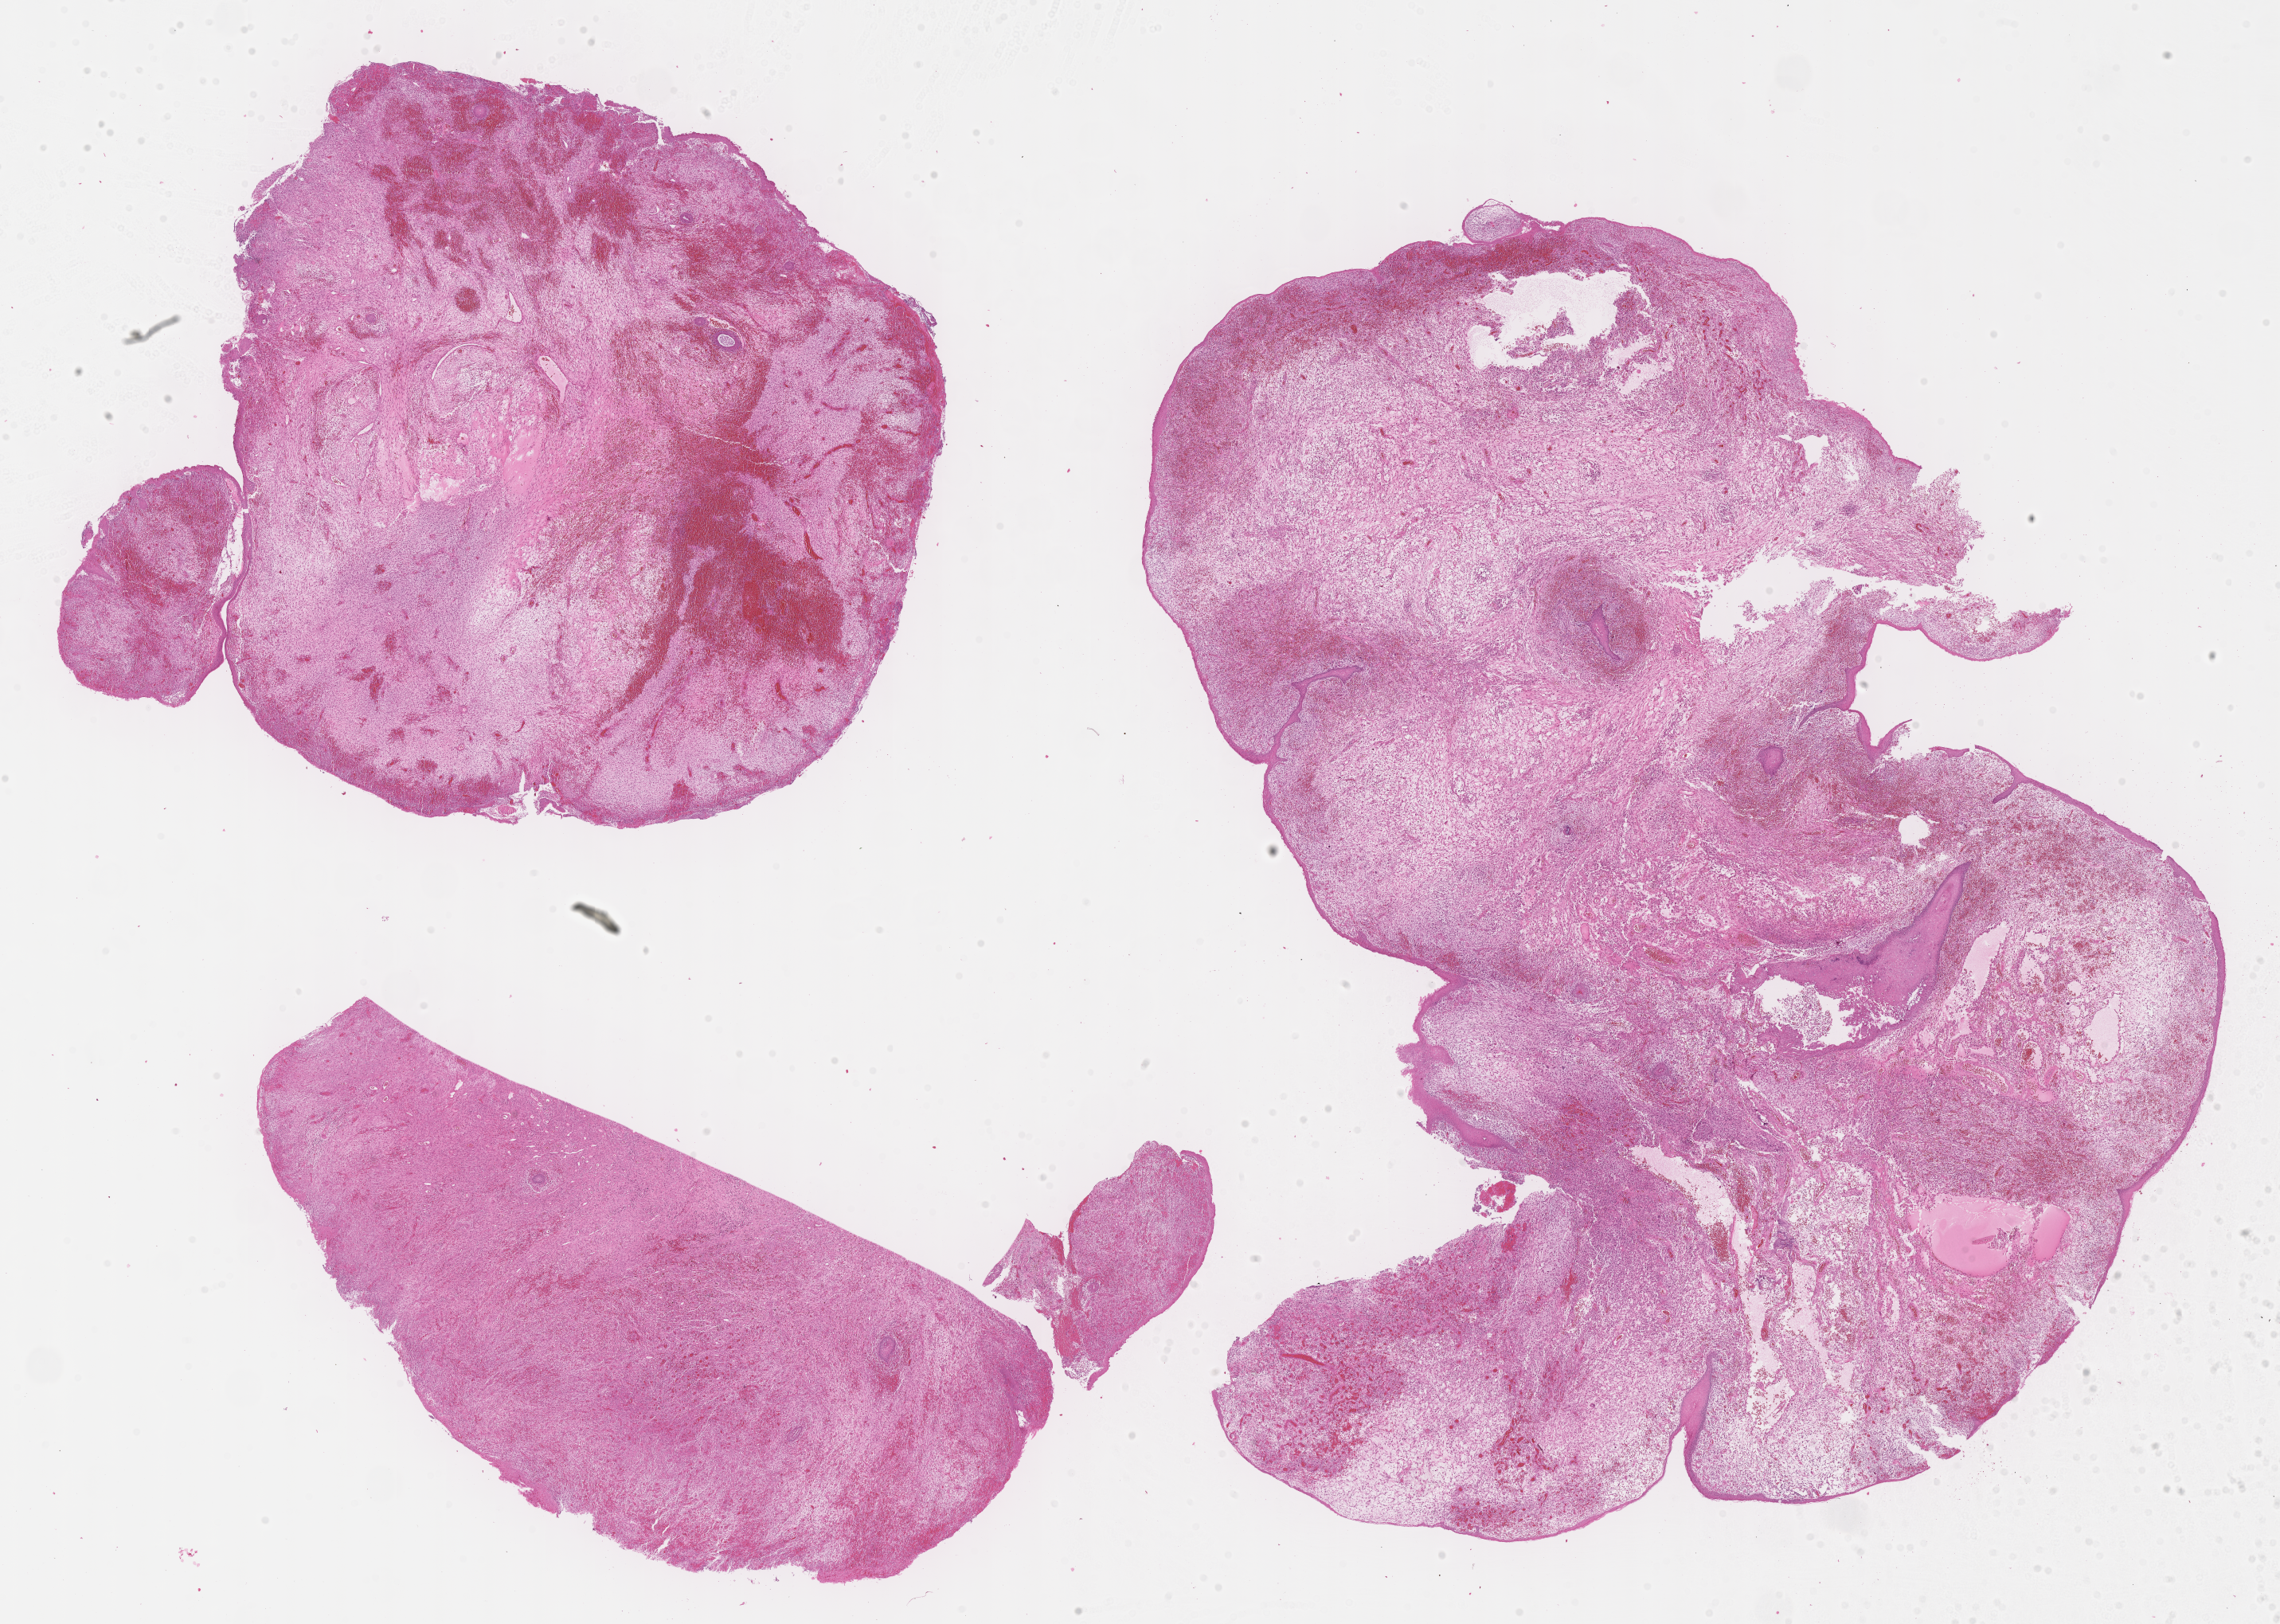
Whole-slide image, H&E stain of tumor tissue, shown as a low-resolution overview of the whole scanned area (about 23.1 x 16.5 mm); FFPE section; site: cervix. Patient: female, age 14.3 years at diagnosis.
Diagnosis: rhabdomyosarcoma; histological classification: embryonal rhabdomyosarcoma. Stage (as recorded): 1. Metastatic status at presentation (as recorded): non-metastatic.